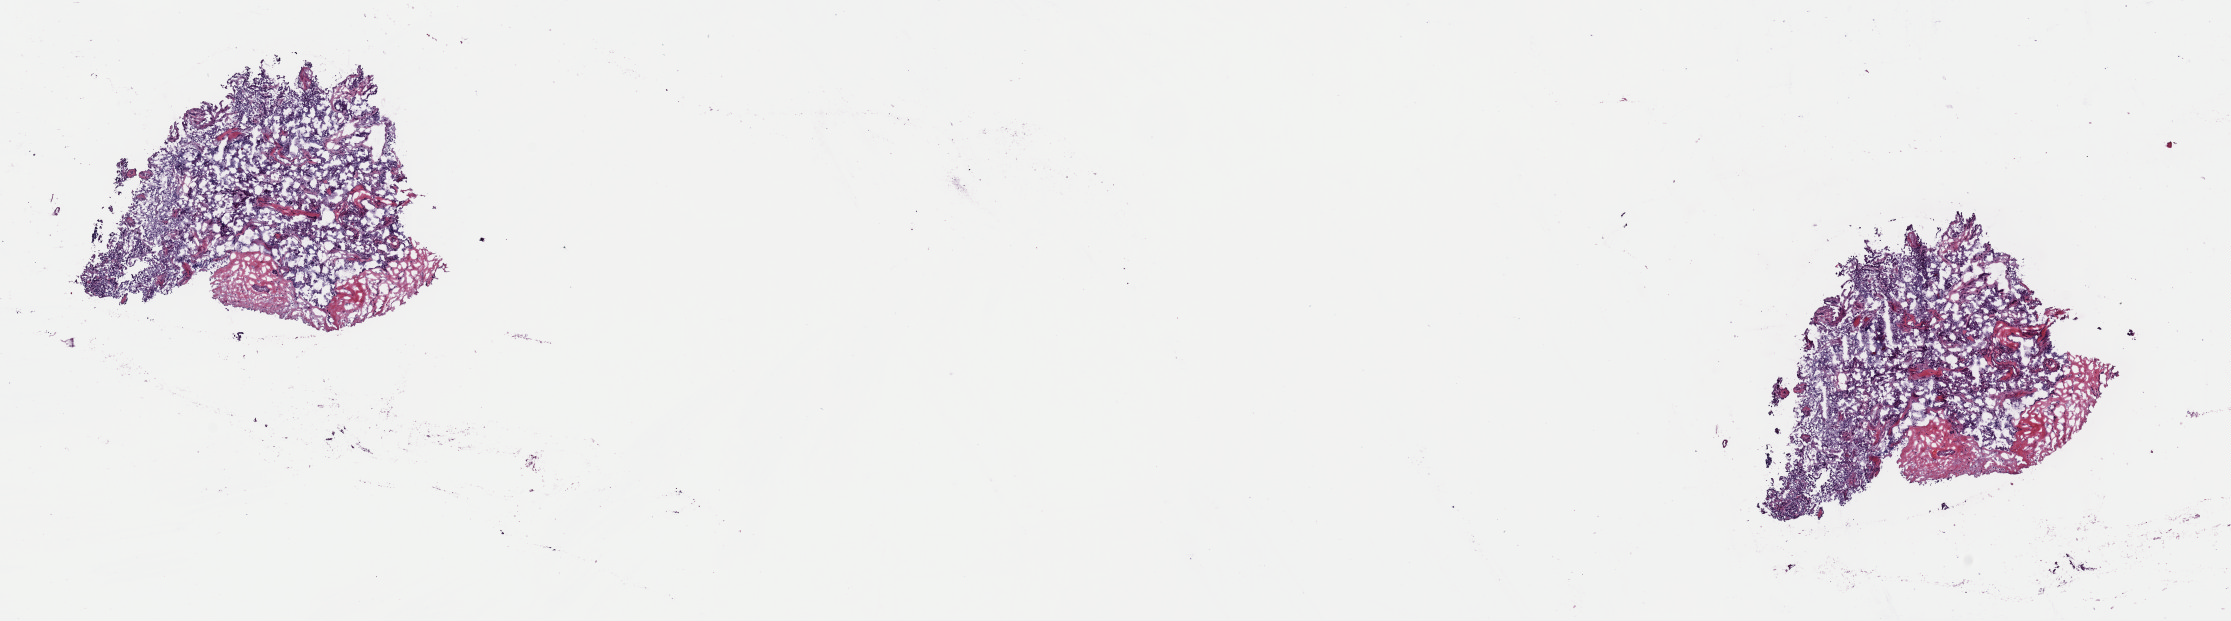
Digitized H&E tissue section (whole slide) — a low-resolution overview of the entire scanned area, about 17.6 x 4.9 mm. Frozen section. Primary tumour sample from the thyroid. Female, age 38 years at initial diagnosis. Slide review estimates, as recorded: tumour cells 85%, tumour nuclei 80%, normal cells 0%, stromal cells 15%, necrosis 0%. Inflammatory infiltration, as recorded: lymphocyte infiltration 2%, monocyte infiltration 1%, neutrophil infiltration 0%.
AJCC pathologic stage: I. Histologic diagnosis: Papillary adenocarcinoma, NOS (thyroid gland).